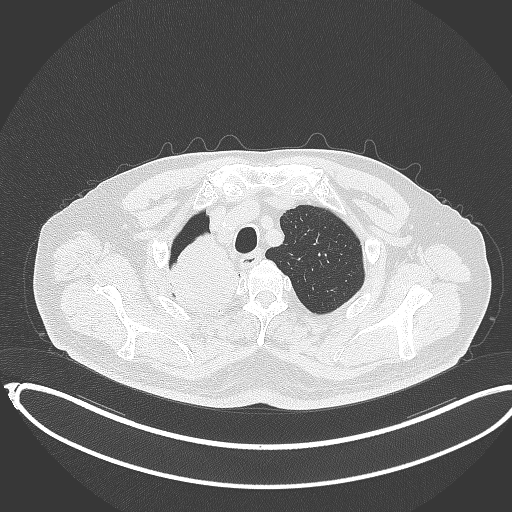
Chest CT, one axial slice. Reconstruction kernel B70f. 120 kVp. Lung window (W 1500 / L -600 HU). 1 mm slice thickness. 512 × 512 image matrix. Male patient, age 68 years. From the clinical record (not read from this slice): clinical TNM (as recorded): T2a N0 M0.
Outlined on this slice (bounding box drawn by a radiologist):
- lung tumour (recorded histology: adenocarcinoma): bounding box <161,232,242,324> (left, top, right, bottom; pixels)